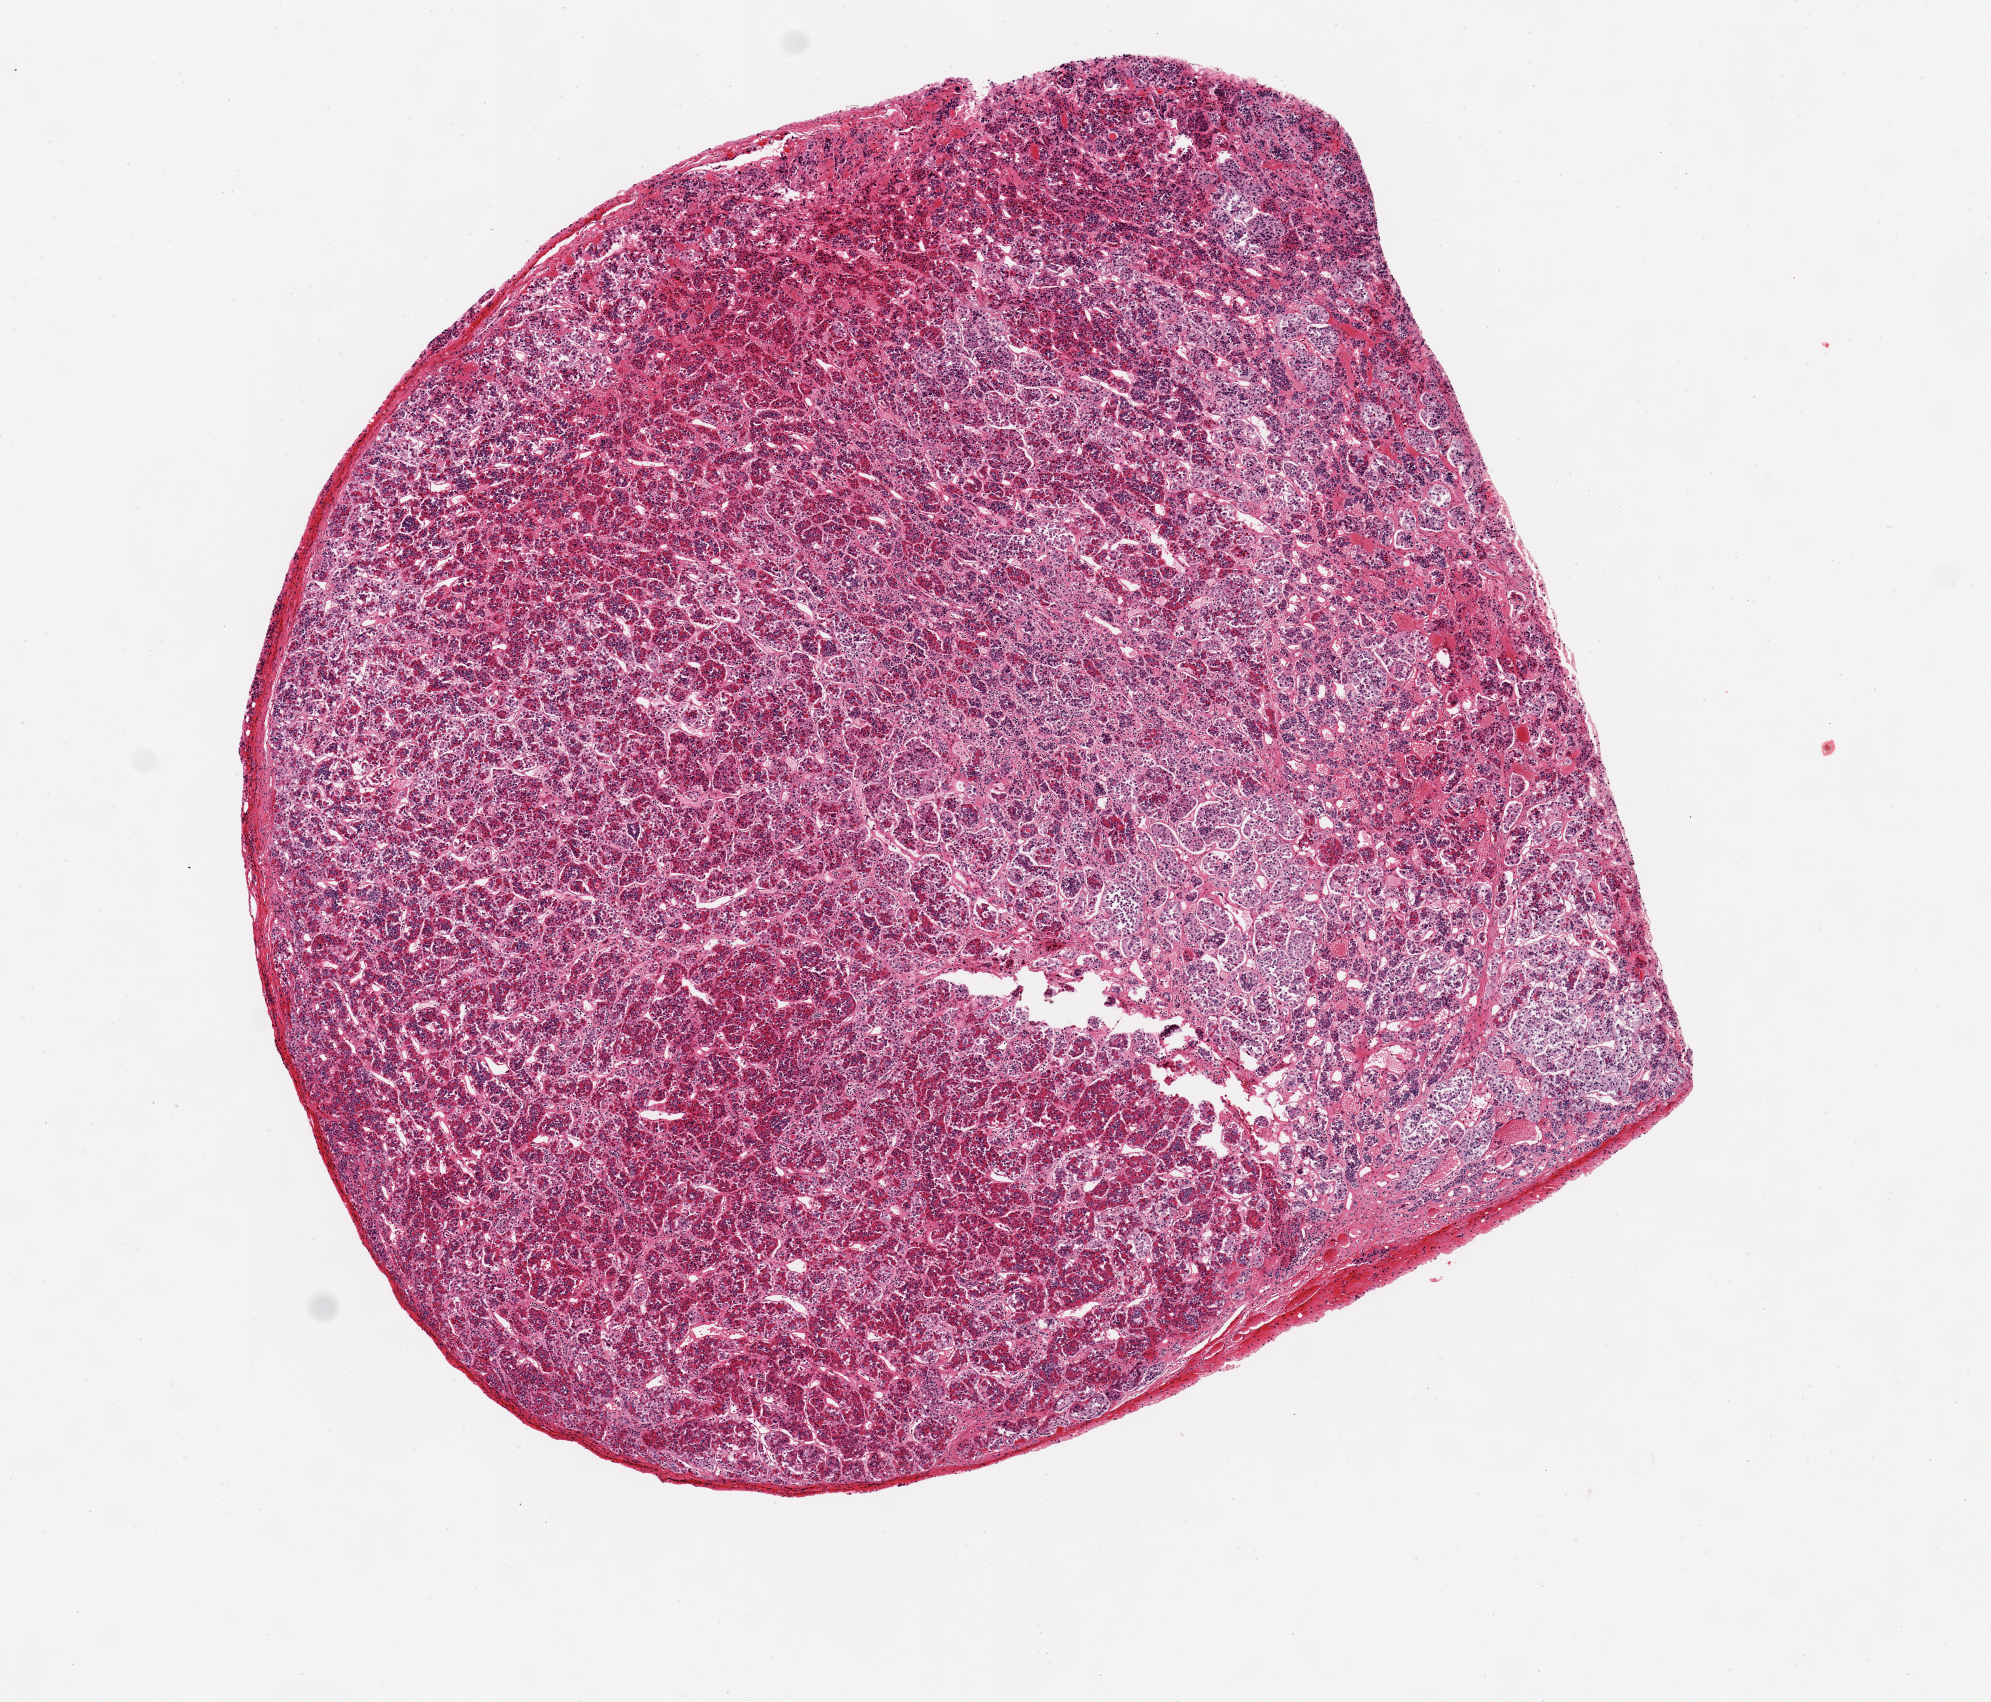
Whole-slide image, H&E stain, brightfield, a low-resolution overview of the entire scanned area, about 7.9 x 6.7 mm; PAXgene-fixed, paraffin-embedded tissue; sampled site (target tissue): pituitary; tissue donor sample. Donor: male.
Reviewer comment on this tissue sample: 1 piece 5x5 mm anterior pituitary.